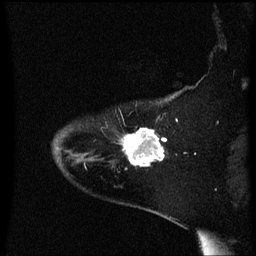
Breast MRI (dynamic contrast-enhanced), one sagittal slice. Position 49 of 60 along the scan axis. Dynamic contrast-enhanced series, image 2 of 3 at this slice position (ordered by acquisition). 1.5 T. TE 4.2 ms, TR 8.4 ms. 2 mm slice thickness. 256 × 256 image matrix. Patient: female, 54 years. Case-level facts recorded for this patient, not image findings: setting: breast cancer imaged before/during neoadjuvant chemotherapy; receptor status: HR-positive, HER2-negative.
Outlined on this slice (semi-automatic segmentation, software-assisted and operator-edited):
- analysis volume of interest (the breast-tissue region the enhancement analysis was run in; not a lesion): bounding box (x1, y1, x2, y2) in pixels: (119, 128, 168, 167)
- tumour enhancement mask (voxels above the 70 % enhancement threshold inside the analysis volume of interest): (122, 128, 167, 167)